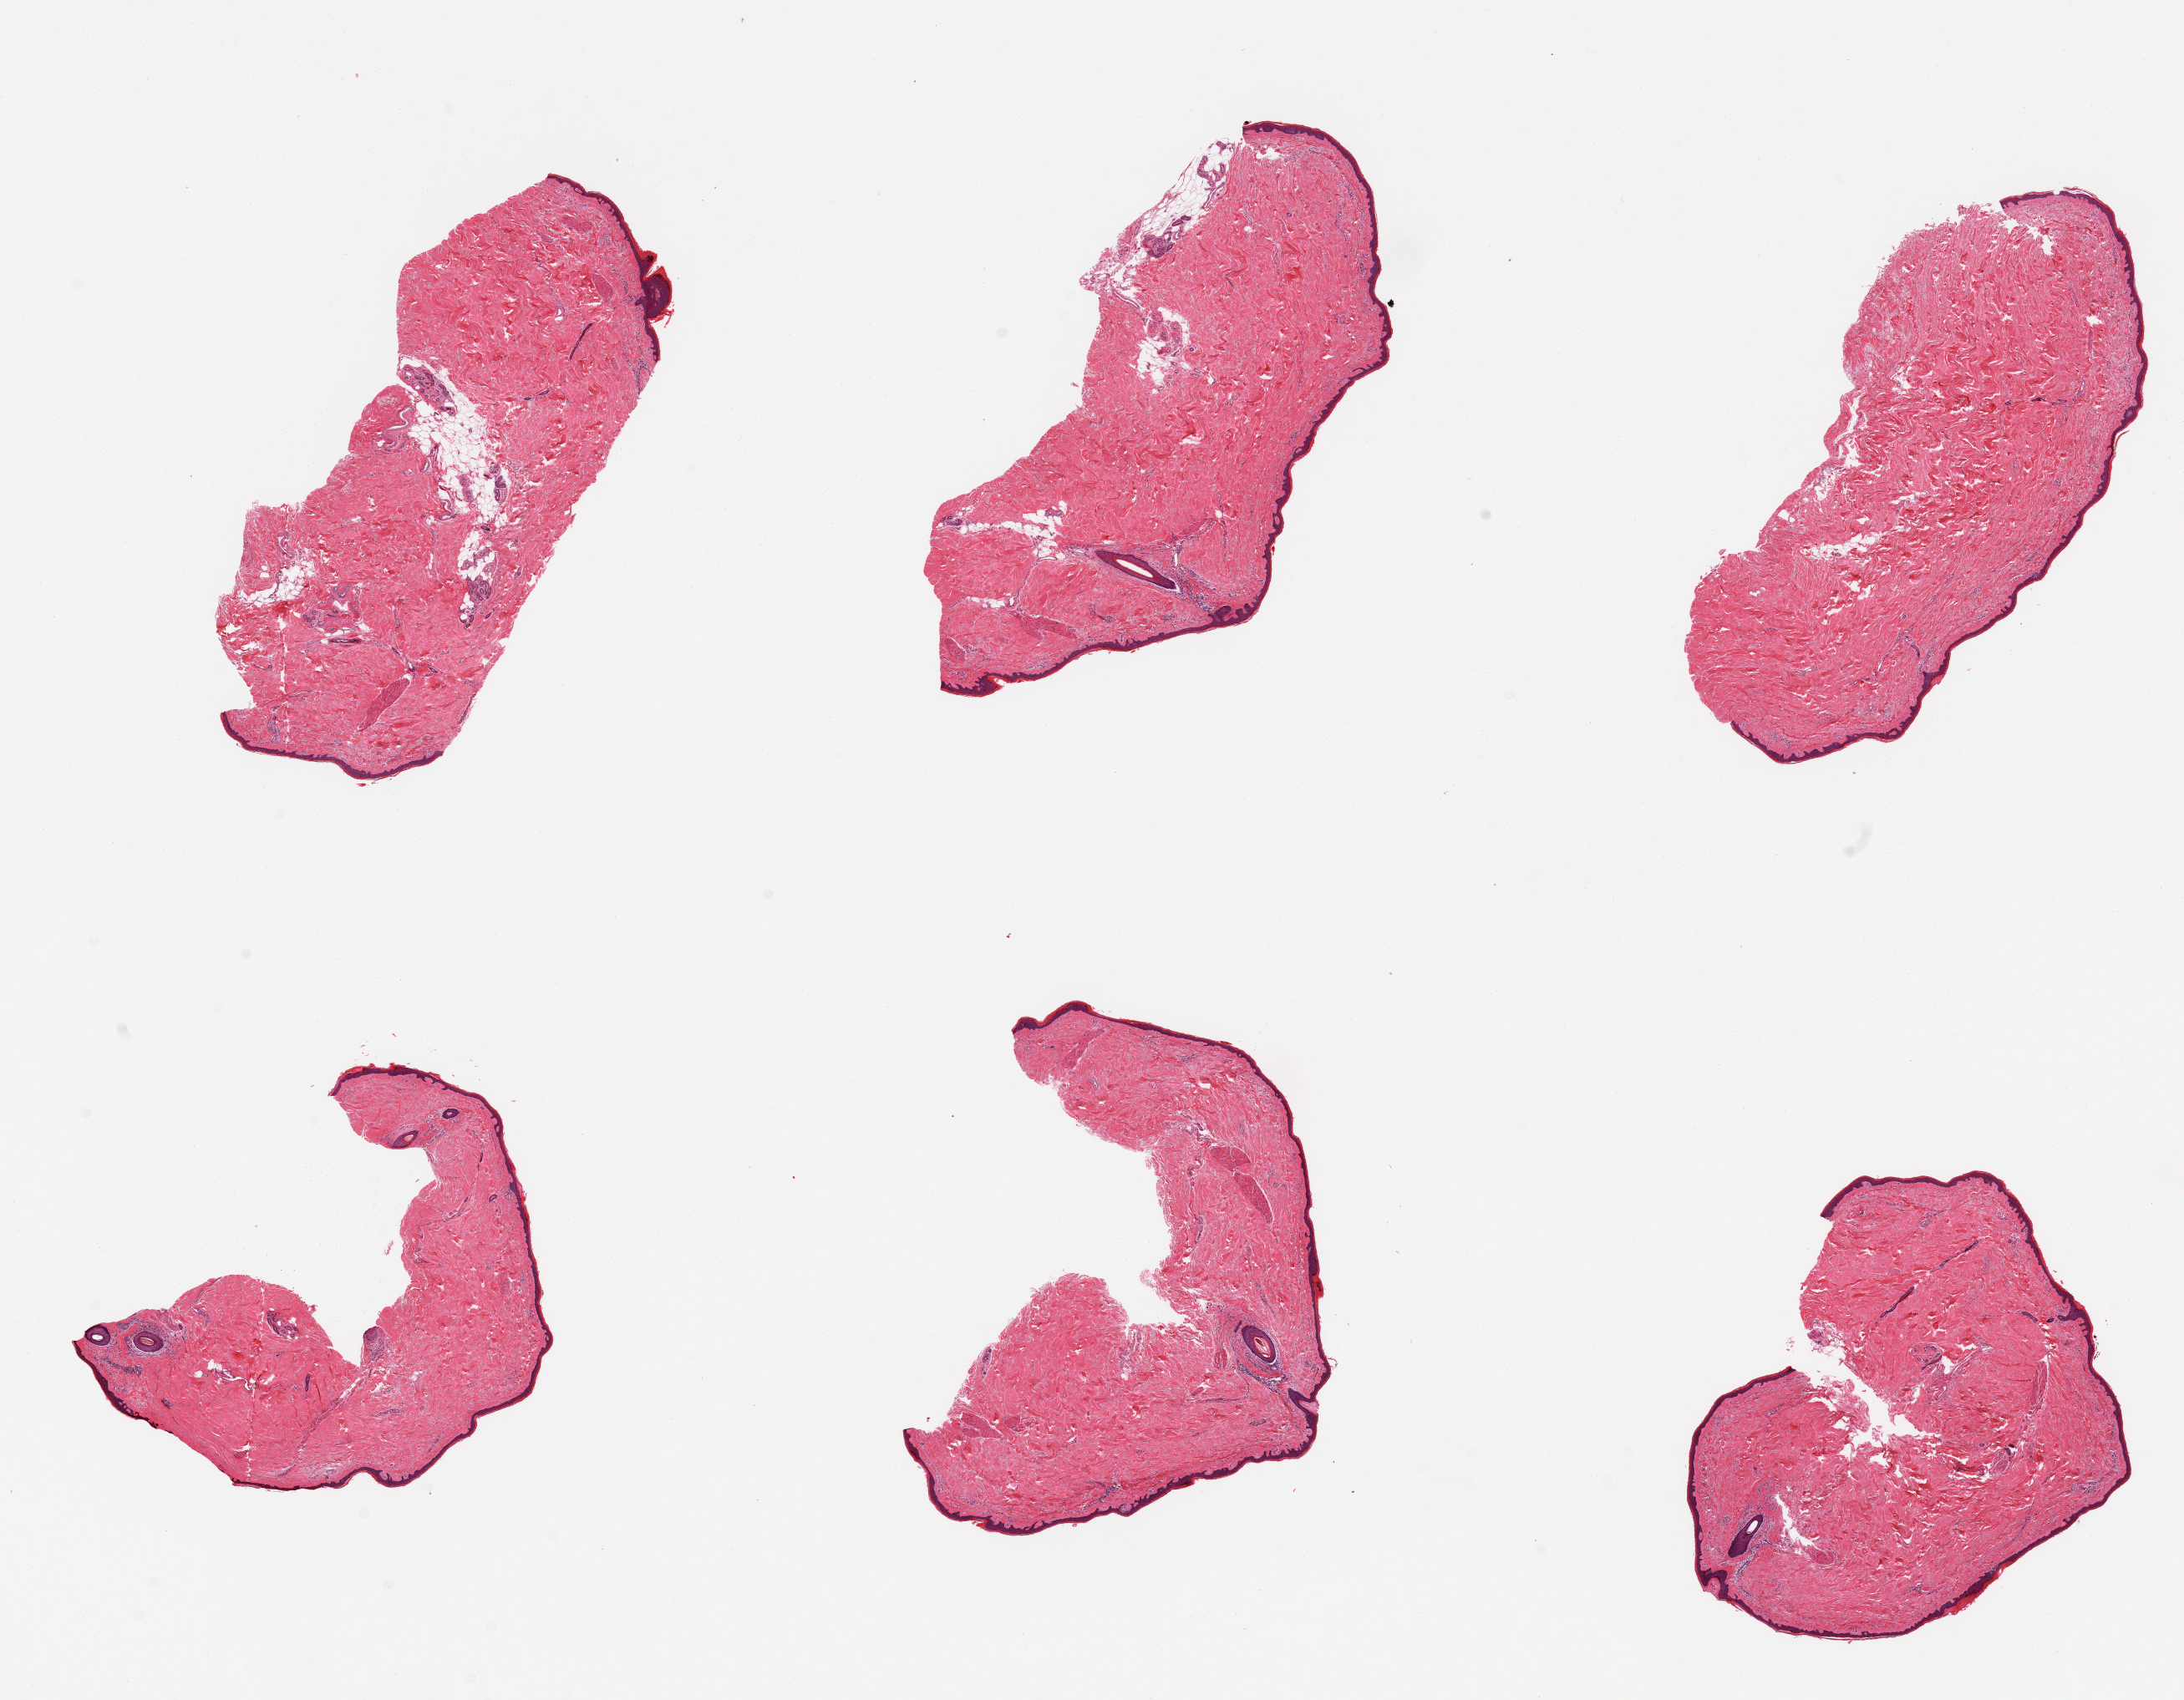
H&E whole-slide image — a low-resolution overview of the entire scanned area, about 20.7 x 16.1 mm. PAXgene-fixed paraffin-embedded (PFPE) section. Section of skin of lower leg (target tissue). Donor tissue sample.
Reviewer comment on this tissue sample: 6 pieces; 5-10% dermal fat; well trimmed.